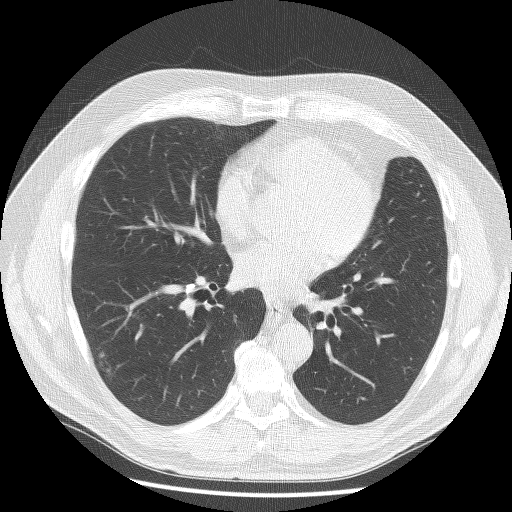
Low-dose screening chest CT, axial slice, first (baseline) screen, lung window (W 1500 / L -600 HU), slice 94 of 179 in the series. Male, age 61 years at enrolment. Former smoker at enrolment.
• Expert reader's lesion annotation, bounding box [x1, y1, x2, y2] px = [81, 340, 135, 394].
• Screening reader's record for this exam (one nodule recorded; not confirmed to be the boxed lesion): non-calcified nodule or mass ≥4 mm, right lower lobe, 10 × 8 mm, spiculated (stellate) margins, soft tissue attenuation.
• Lung cancer was diagnosed 407 days after this screen: adenosquamous carcinoma, right lower lobe, poorly differentiated (G3), stage IV (AJCC 6th edition), 45 mm at pathology.